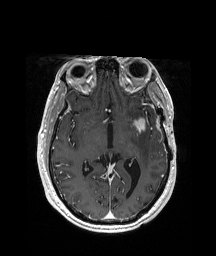
Brain MRI from a brain-tumour surgery series, one axial slice; T1-weighted post-contrast; 216 × 256 image matrix. Case-level facts recorded for this patient, not image findings: histopathology: Glioblastoma; WHO grade: 4; IDH mutation: no.
Annotated regions visible in this slice (outlined manually by an expert reader):
- tumour: box from (x=123, y=117) to (x=158, y=132) px